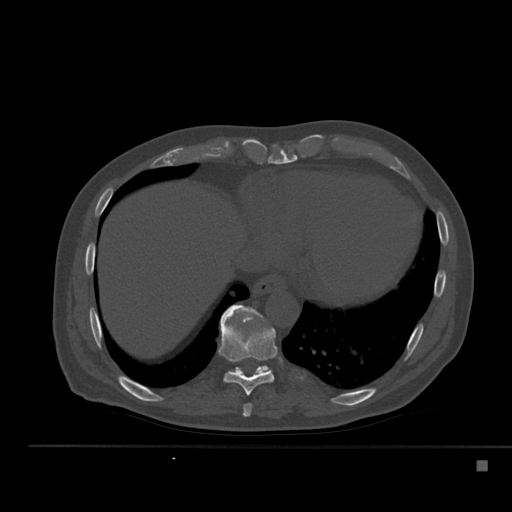
CT including the spine, one axial slice; slice 285 of 517 in the series (ordered by position); reconstruction kernel Br40s; bone window (W 1800 / L 400 HU); 1.5 mm slice thickness; 512 × 512 image matrix, field of view 408 × 408 mm. Patient: male, 70 years. From the clinical record (not read from this slice): primary cancer: renal; vertebrae with lytic lesions (as recorded): T4, T6, T10, T12, L3, L4, L5.
Structures marked on this image (semi-automatic segmentation, software-assisted and operator-edited):
- T10 vertebra: bounding box <222,305,269,375> (left, top, right, bottom; pixels)
- T8 vertebra: <243,403,252,417>
- T9 vertebra: <218,316,277,396>